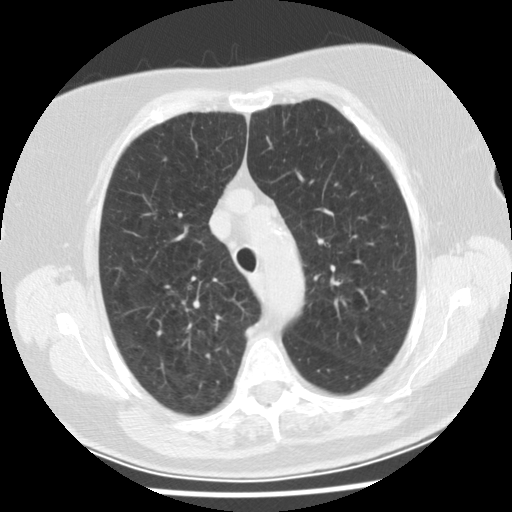
Chest CT (low-dose screening protocol), one axial image, first (baseline) screen, lung window (W 1500 / L -600 HU), 2.5 mm slice thickness, standard (soft-tissue) reconstruction kernel (STANDARD). Female participant, aged 74 years at enrolment. Former smoker at enrolment.
• Expert-annotated lung lesion, bounding box [x1, y1, x2, y2] px = [309, 118, 345, 145].
• The screening reader recorded 2 non-calcified nodules or masses ≥4 mm on this exam (left upper lobe, left lower lobe); which of them this box marks is not recorded.
• Lung cancer was diagnosed 532 days after this screen (after the second annual screen): bronchiolo-alveolar adenocarcinoma, NOS, left upper lobe, stage IA (AJCC 6th edition), 20 mm at pathology.